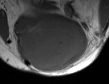
MRI of an extremity soft-tissue mass, one axial slice. Slice 23 of 50 in the series (ordered by position). MR volume resampled by the dataset authors to the PET/CT grid (not the native acquisition matrix). 109 × 84 image matrix, field of view 106 × 82 mm. Male patient. Case-level facts recorded for this patient, not image findings: histological type: synovial sarcoma; site of the primary tumour: left poplietal fossa.
Outlined on this slice (expert contour drawn on MRI and transferred to this co-registered scan by the dataset authors):
- gross tumour volume (mass): bounding box [x1, y1, x2, y2] px = [16, 17, 88, 72]